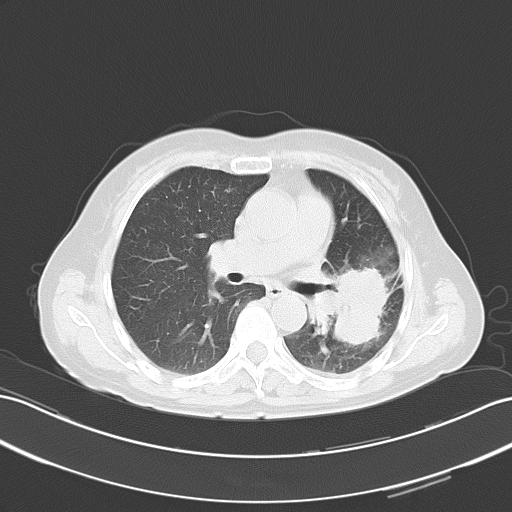
Chest CT, one axial slice. Position 29 of 51 along the scan axis. 120 kVp. Lung window (W 1500 / L -600 HU). 5 mm slice thickness. 512 × 512 image matrix. Patient: female, 54 years. Case-level facts recorded for this patient, not image findings: clinical TNM (as recorded): T3 N1 M0.
Structures marked on this image (rectangle marked by the reading radiologist):
- lung tumour (recorded histology: adenocarcinoma): bounding box <325,268,389,355> (left, top, right, bottom; pixels)